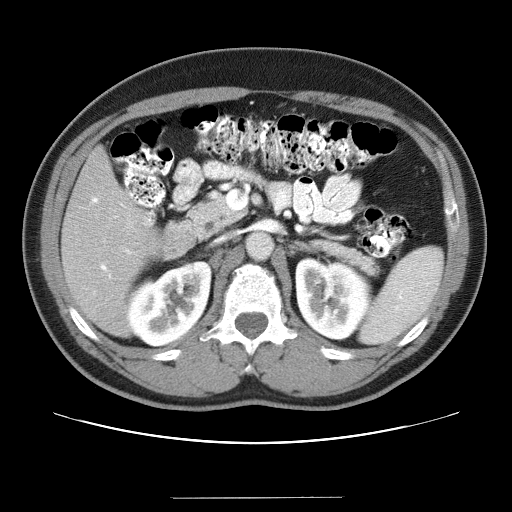
Contrast-enhanced abdominal CT (liver protocol), one axial slice. Position 13 of 40 along the scan axis. Reconstruction kernel STANDARD. Soft-tissue window (W 400 / L 40 HU). 5 mm slice thickness. 512 × 512 image matrix, field of view 380 × 380 mm. From the clinical record (not read from this slice): diagnosis: hepatocellular carcinoma (patient treated with transarterial chemoembolisation; whether this scan precedes or follows treatment is not stated here); TNM stage (as recorded): Stage-IVA; Child-Pugh class: B; tumour nodularity: multinodular.
Outlined on this slice (semi-automatically segmented with operator editing):
- liver parenchyma outside the tumour (the mass and vessels are separate outlines, so this box may not span the whole liver): bounding box (x1, y1, x2, y2) in pixels: (62, 146, 158, 336)
- liver vessels: (91, 197, 152, 294)